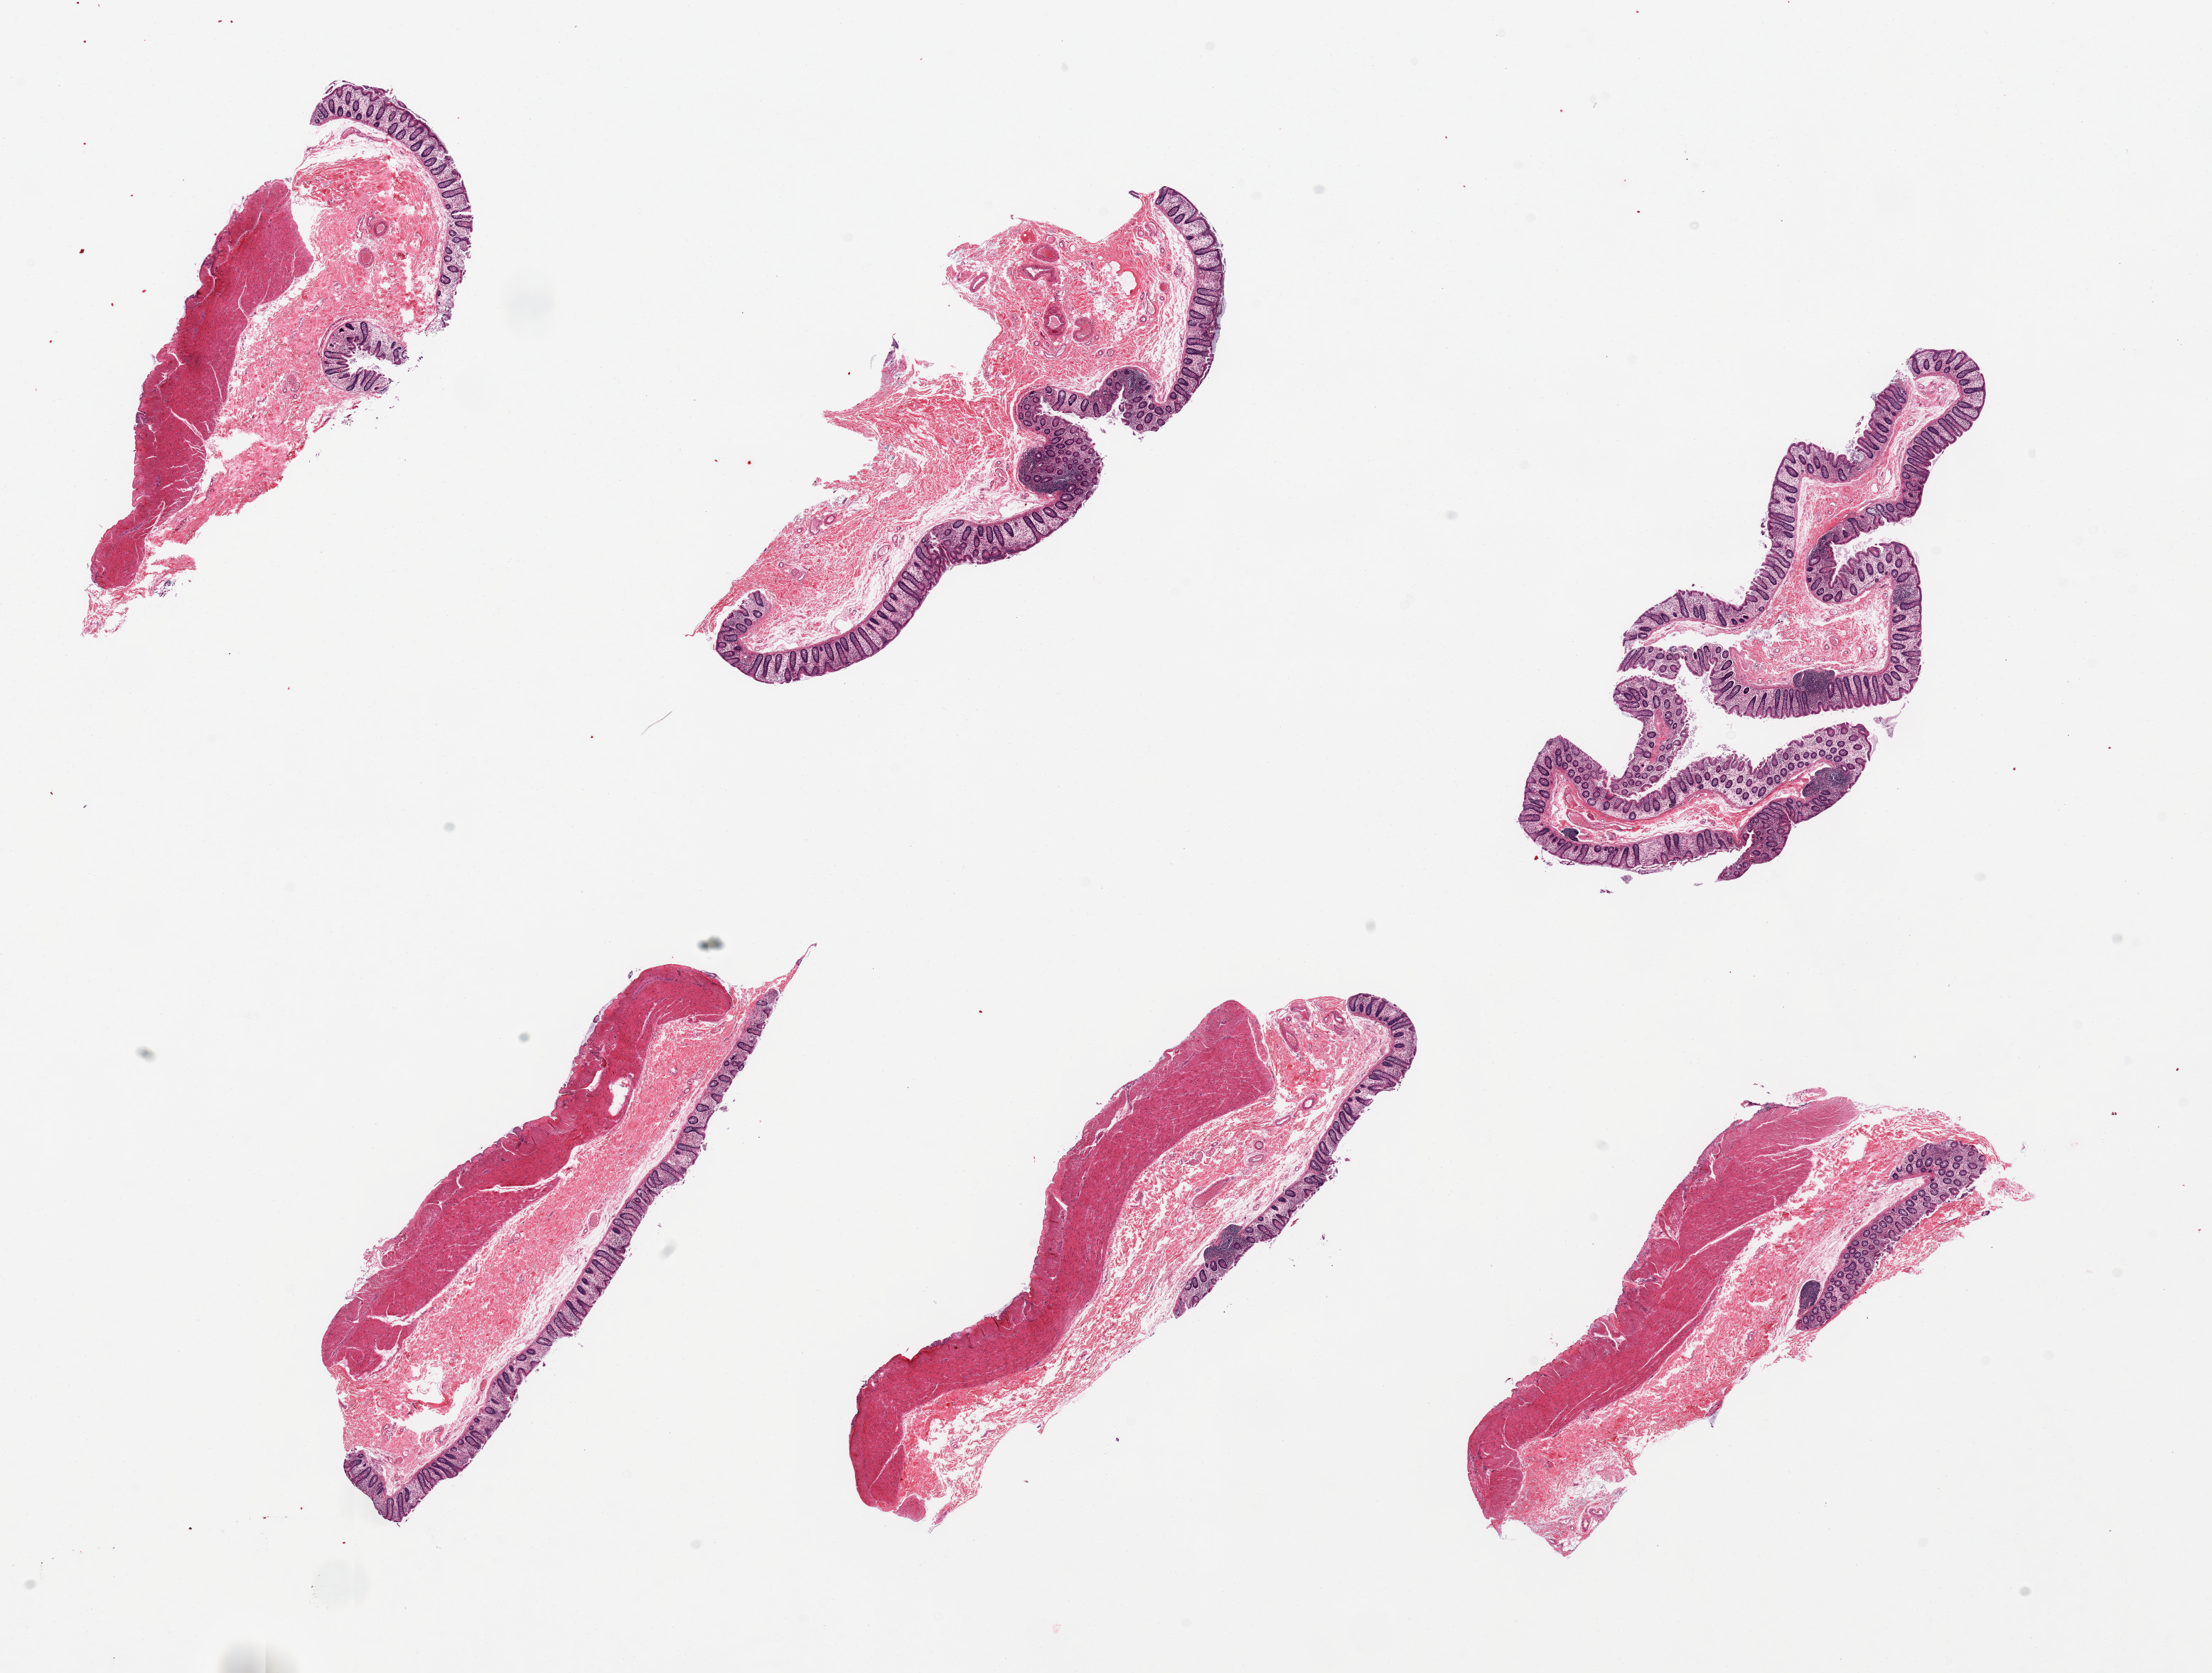
Haematoxylin and eosin whole-slide image, brightfield — shown as a low-resolution overview of the whole scanned area (about 24.6 x 18.6 mm, from a 20x scan); PAXgene-fixed, paraffin-embedded tissue; sampled site (target tissue): transverse colon; donor tissue sample. Female donor.
Pathologist's review note for this sample: 6 pieces, mucosa and muscularis.